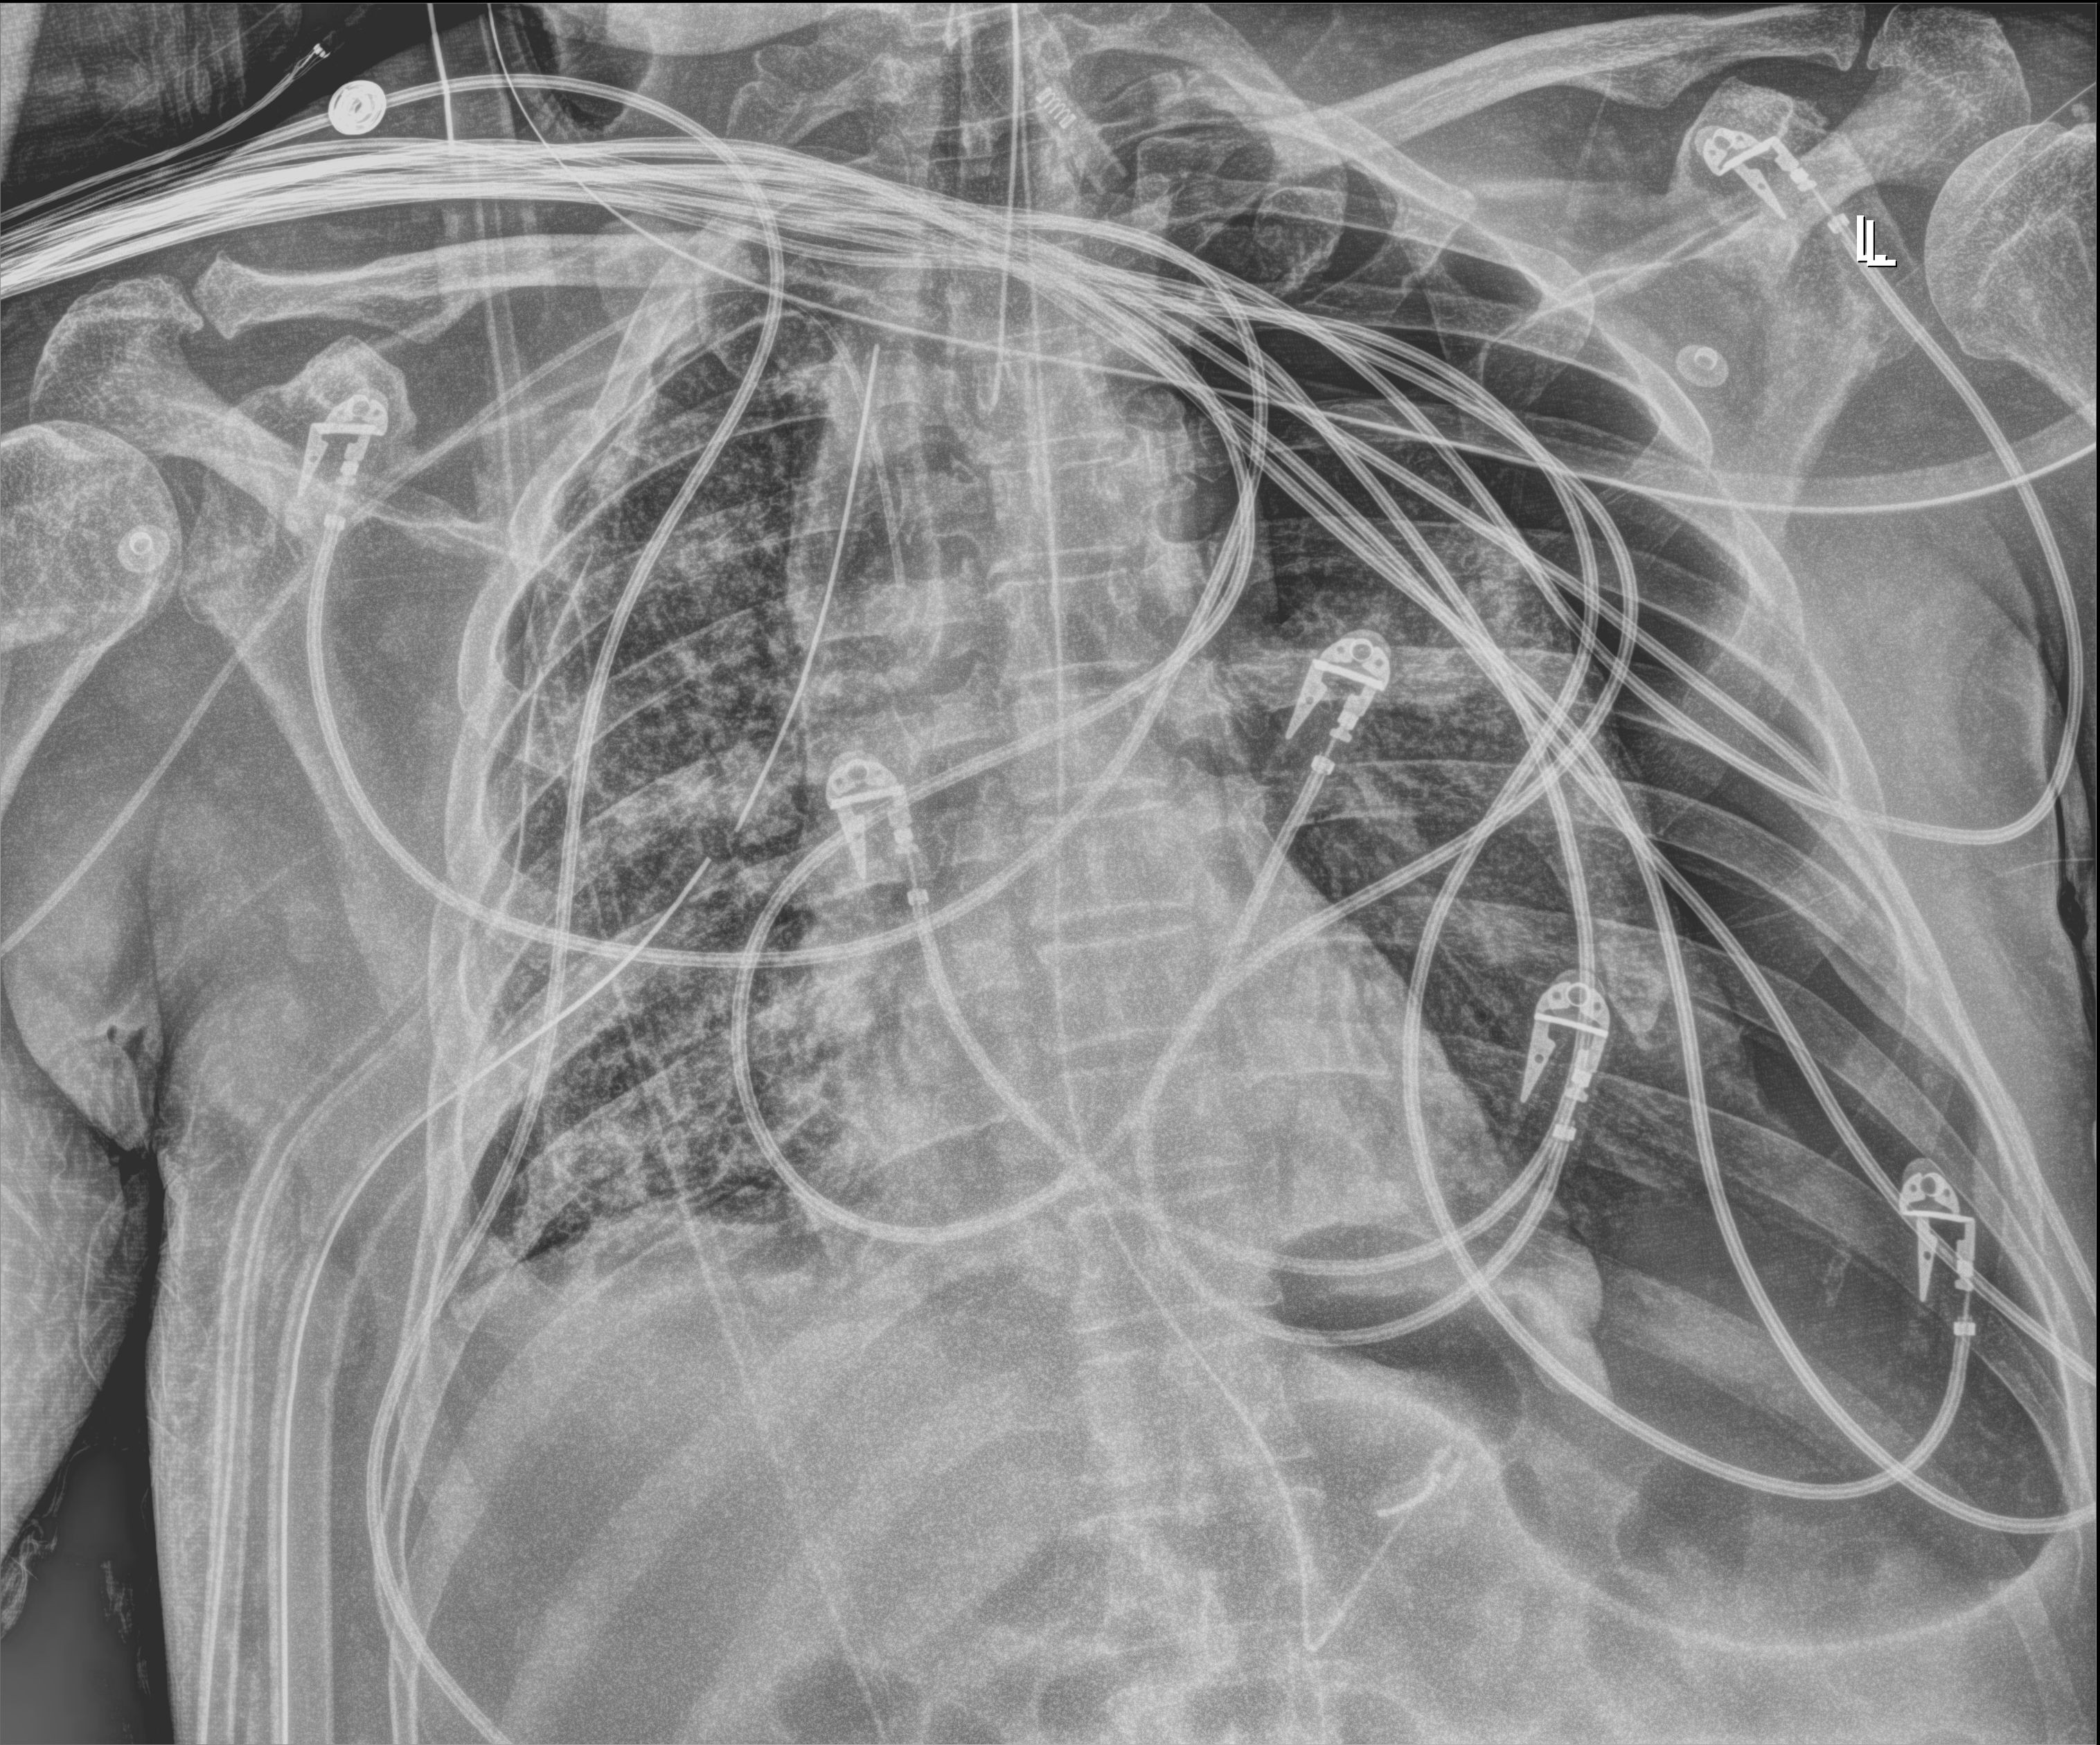
Bedside chest radiograph (digital radiography); anteroposterior (AP) projection. Patient hospitalised with COVID-19; male, aged 60–74 years.
From the hospital-stay record, not from the radiograph (when in the stay this image was taken is not recorded):
- mechanically ventilated during this hospital stay: yes